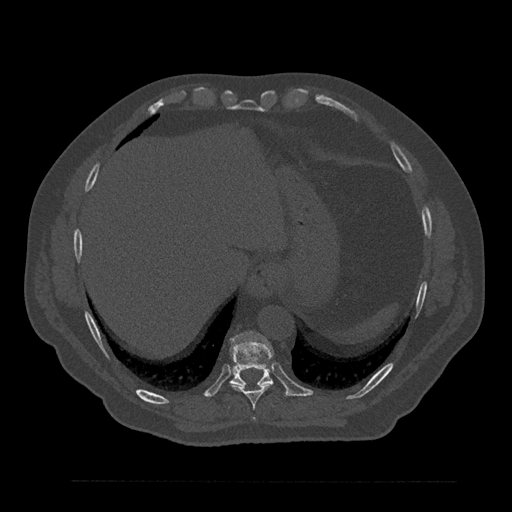
CT including the spine, one axial slice; position 381 of 797 along the scan axis; 120 kVp; bone window (W 1800 / L 400 HU); 512 × 512 image matrix, field of view 430 × 430 mm. Male patient, age 61 years. From the clinical record (not read from this slice): primary cancer: prostate.
Outlined on this slice (semi-automatically segmented with operator editing):
- T10 vertebra: box from (x=229, y=331) to (x=273, y=385) px
- T8 vertebra: (x=253, y=418)–(x=255, y=421)
- T9 vertebra: (x=231, y=382)–(x=273, y=410)